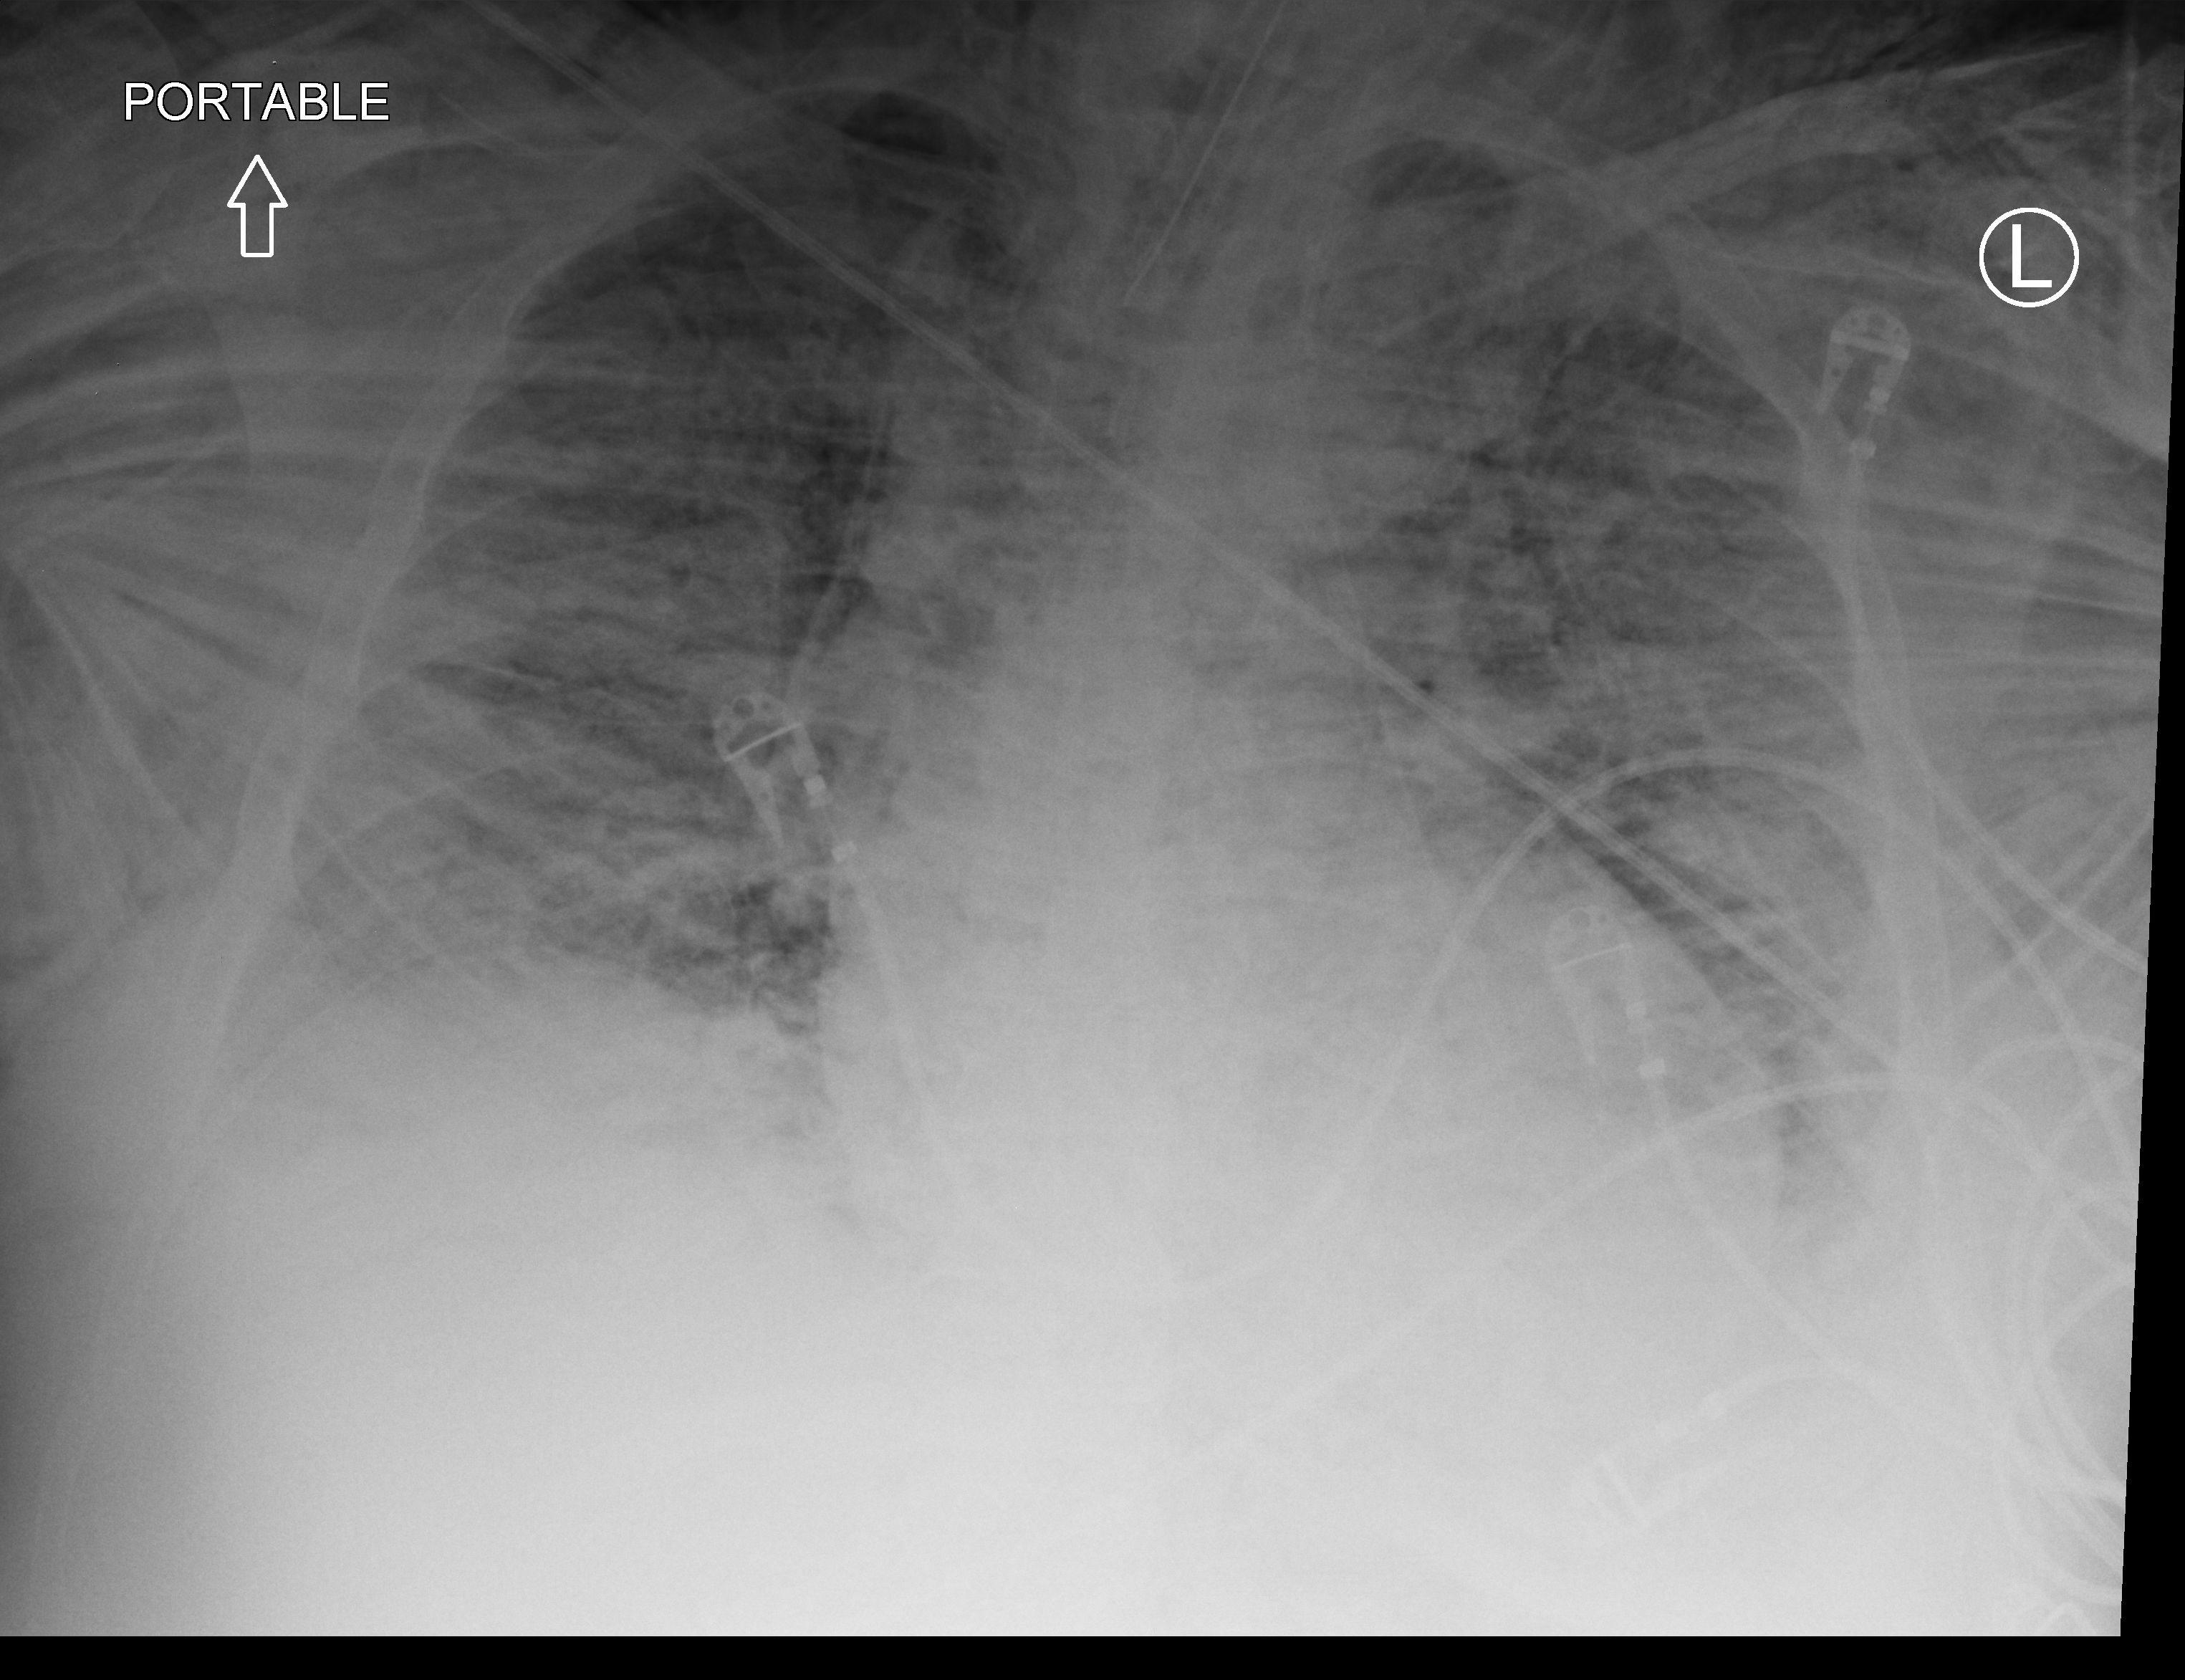
Chest X-ray (portable); anteroposterior (AP) projection. Adult patient hospitalised with COVID-19, age 18–59 years.
From the hospital-stay record, not from the radiograph (when in the stay this image was taken is not recorded):
- mechanically ventilated during this hospital stay: yes
- hypertension (admission record): yes